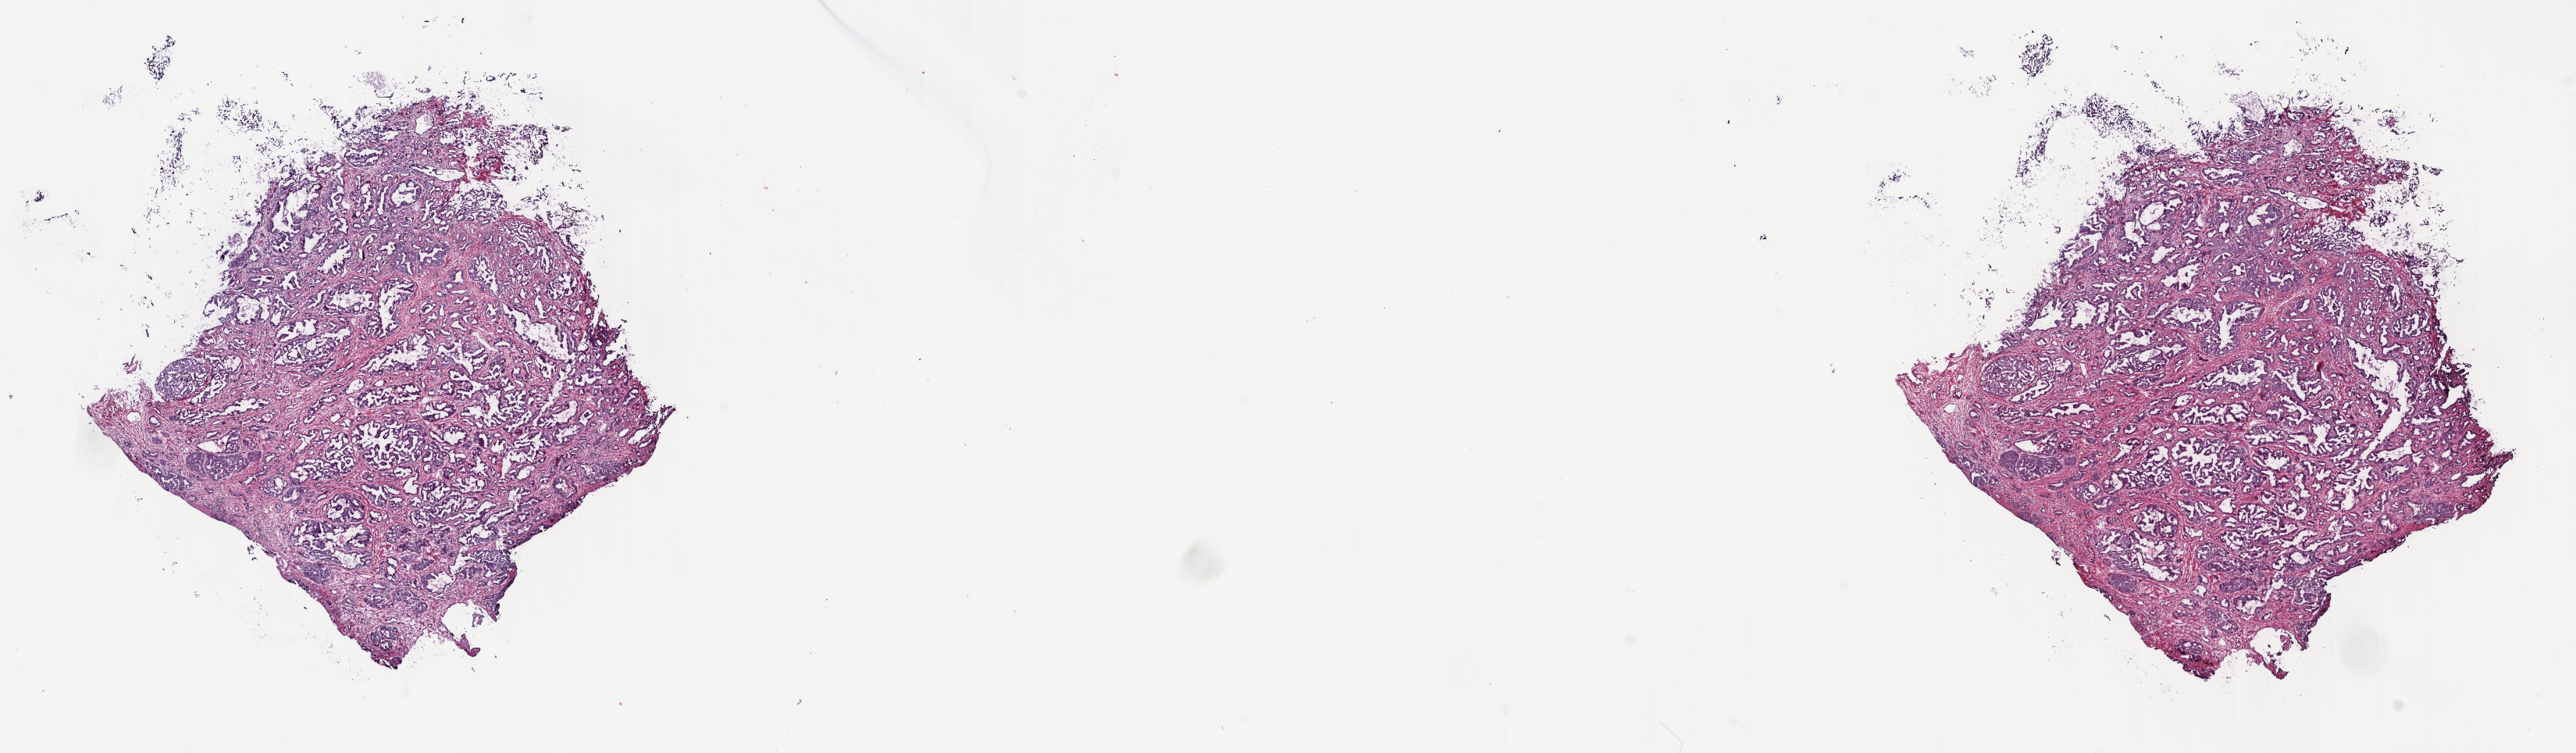
Whole-slide histology image, Hematoxylin and eosin (H&E) stained, shown as a low-resolution overview of the whole scanned area (about 26.7 x 7.8 mm, acquisition: 40x scan). Frozen section. Prostate, primary tumour sample. Male patient; age at initial diagnosis 61 years. Gleason score: 9 (4+5). Composition of this section per pathologist review: tumour cells 65%, tumour nuclei 80%, normal cells 5%, stromal cells 30%, necrosis 0%. Infiltration values recorded for this section: lymphocyte infiltration 0%, monocyte infiltration 0%, neutrophil infiltration 0%.
Histologic diagnosis: Infiltrating duct carcinoma, NOS. Laterality: bilateral.